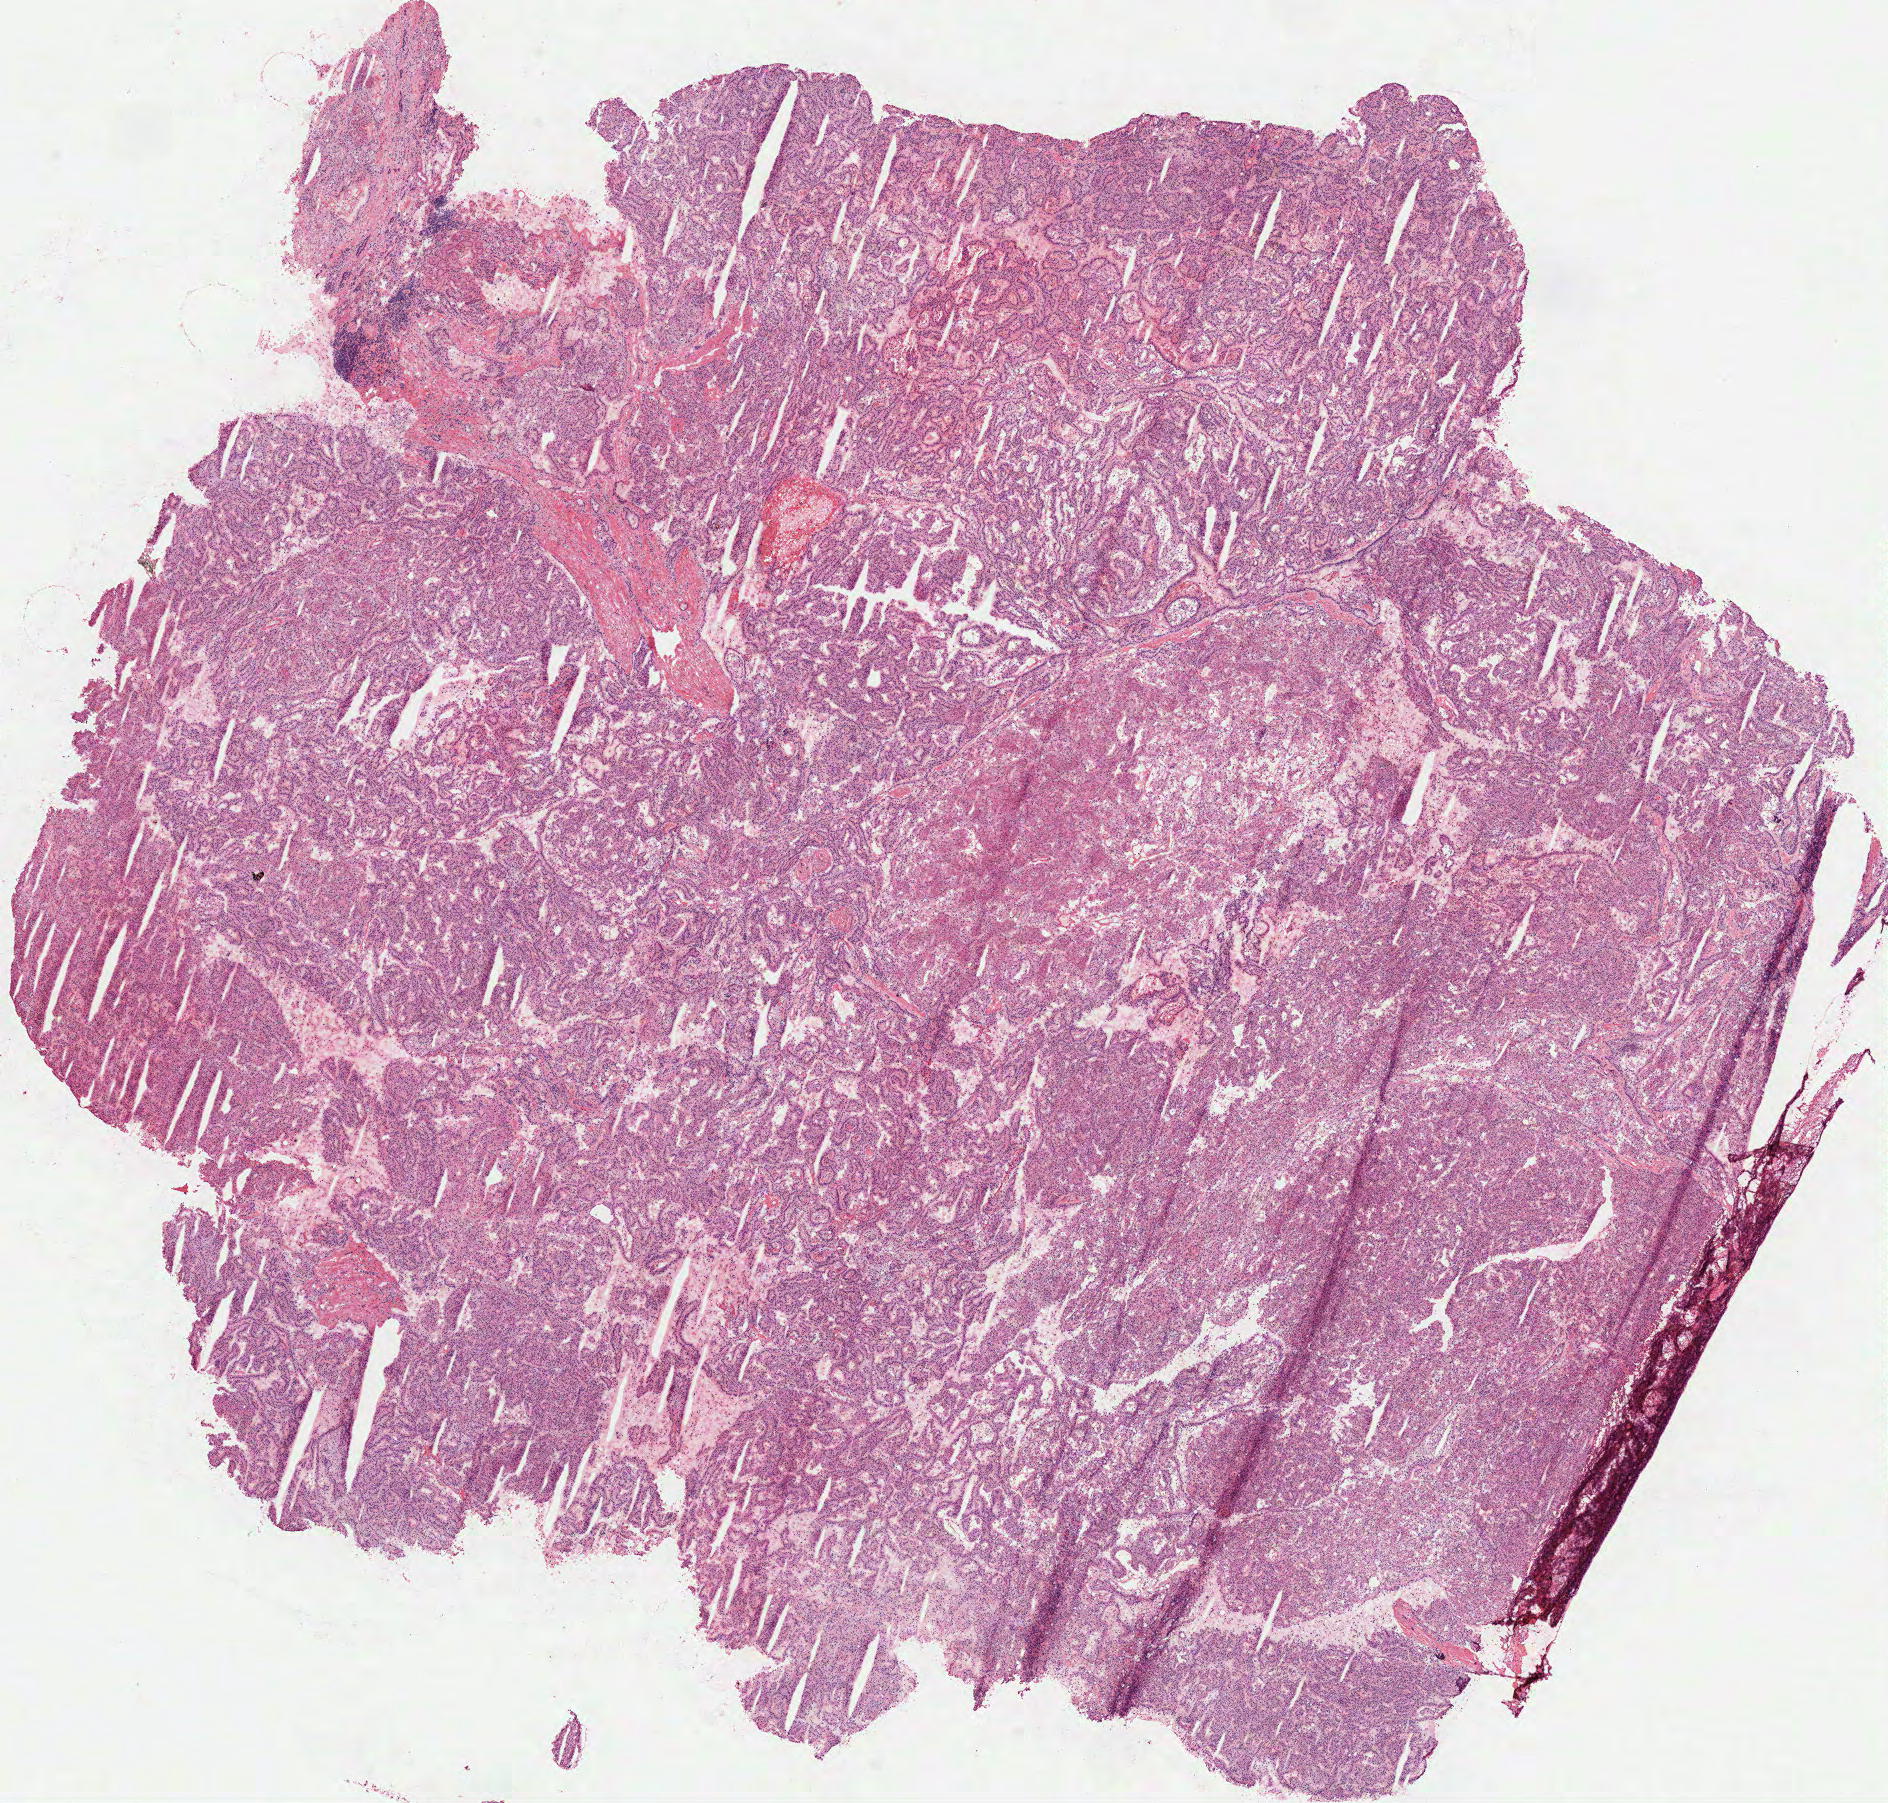
Digitized Hematoxylin and eosin (H&E) stained tissue section (whole slide), a low-resolution overview of the entire scanned area, about 15.2 x 14.5 mm (acquisition: 40x scan). Frozen section from the top of the tissue portion. Sample: primary tumour, kidney. Patient: female, age at initial diagnosis 53 years. Slide review estimates, as recorded: tumour cells 100%, tumour nuclei 85%, normal cells 0%, stromal cells 0%, necrosis 0%. Infiltration values recorded for this section: lymphocyte infiltration 5%, monocyte infiltration 4%, neutrophil infiltration 0%.
Diagnosis: Papillary adenocarcinoma, NOS. TNM: T1a N0 M0. AJCC pathologic stage: I. Laterality: left.